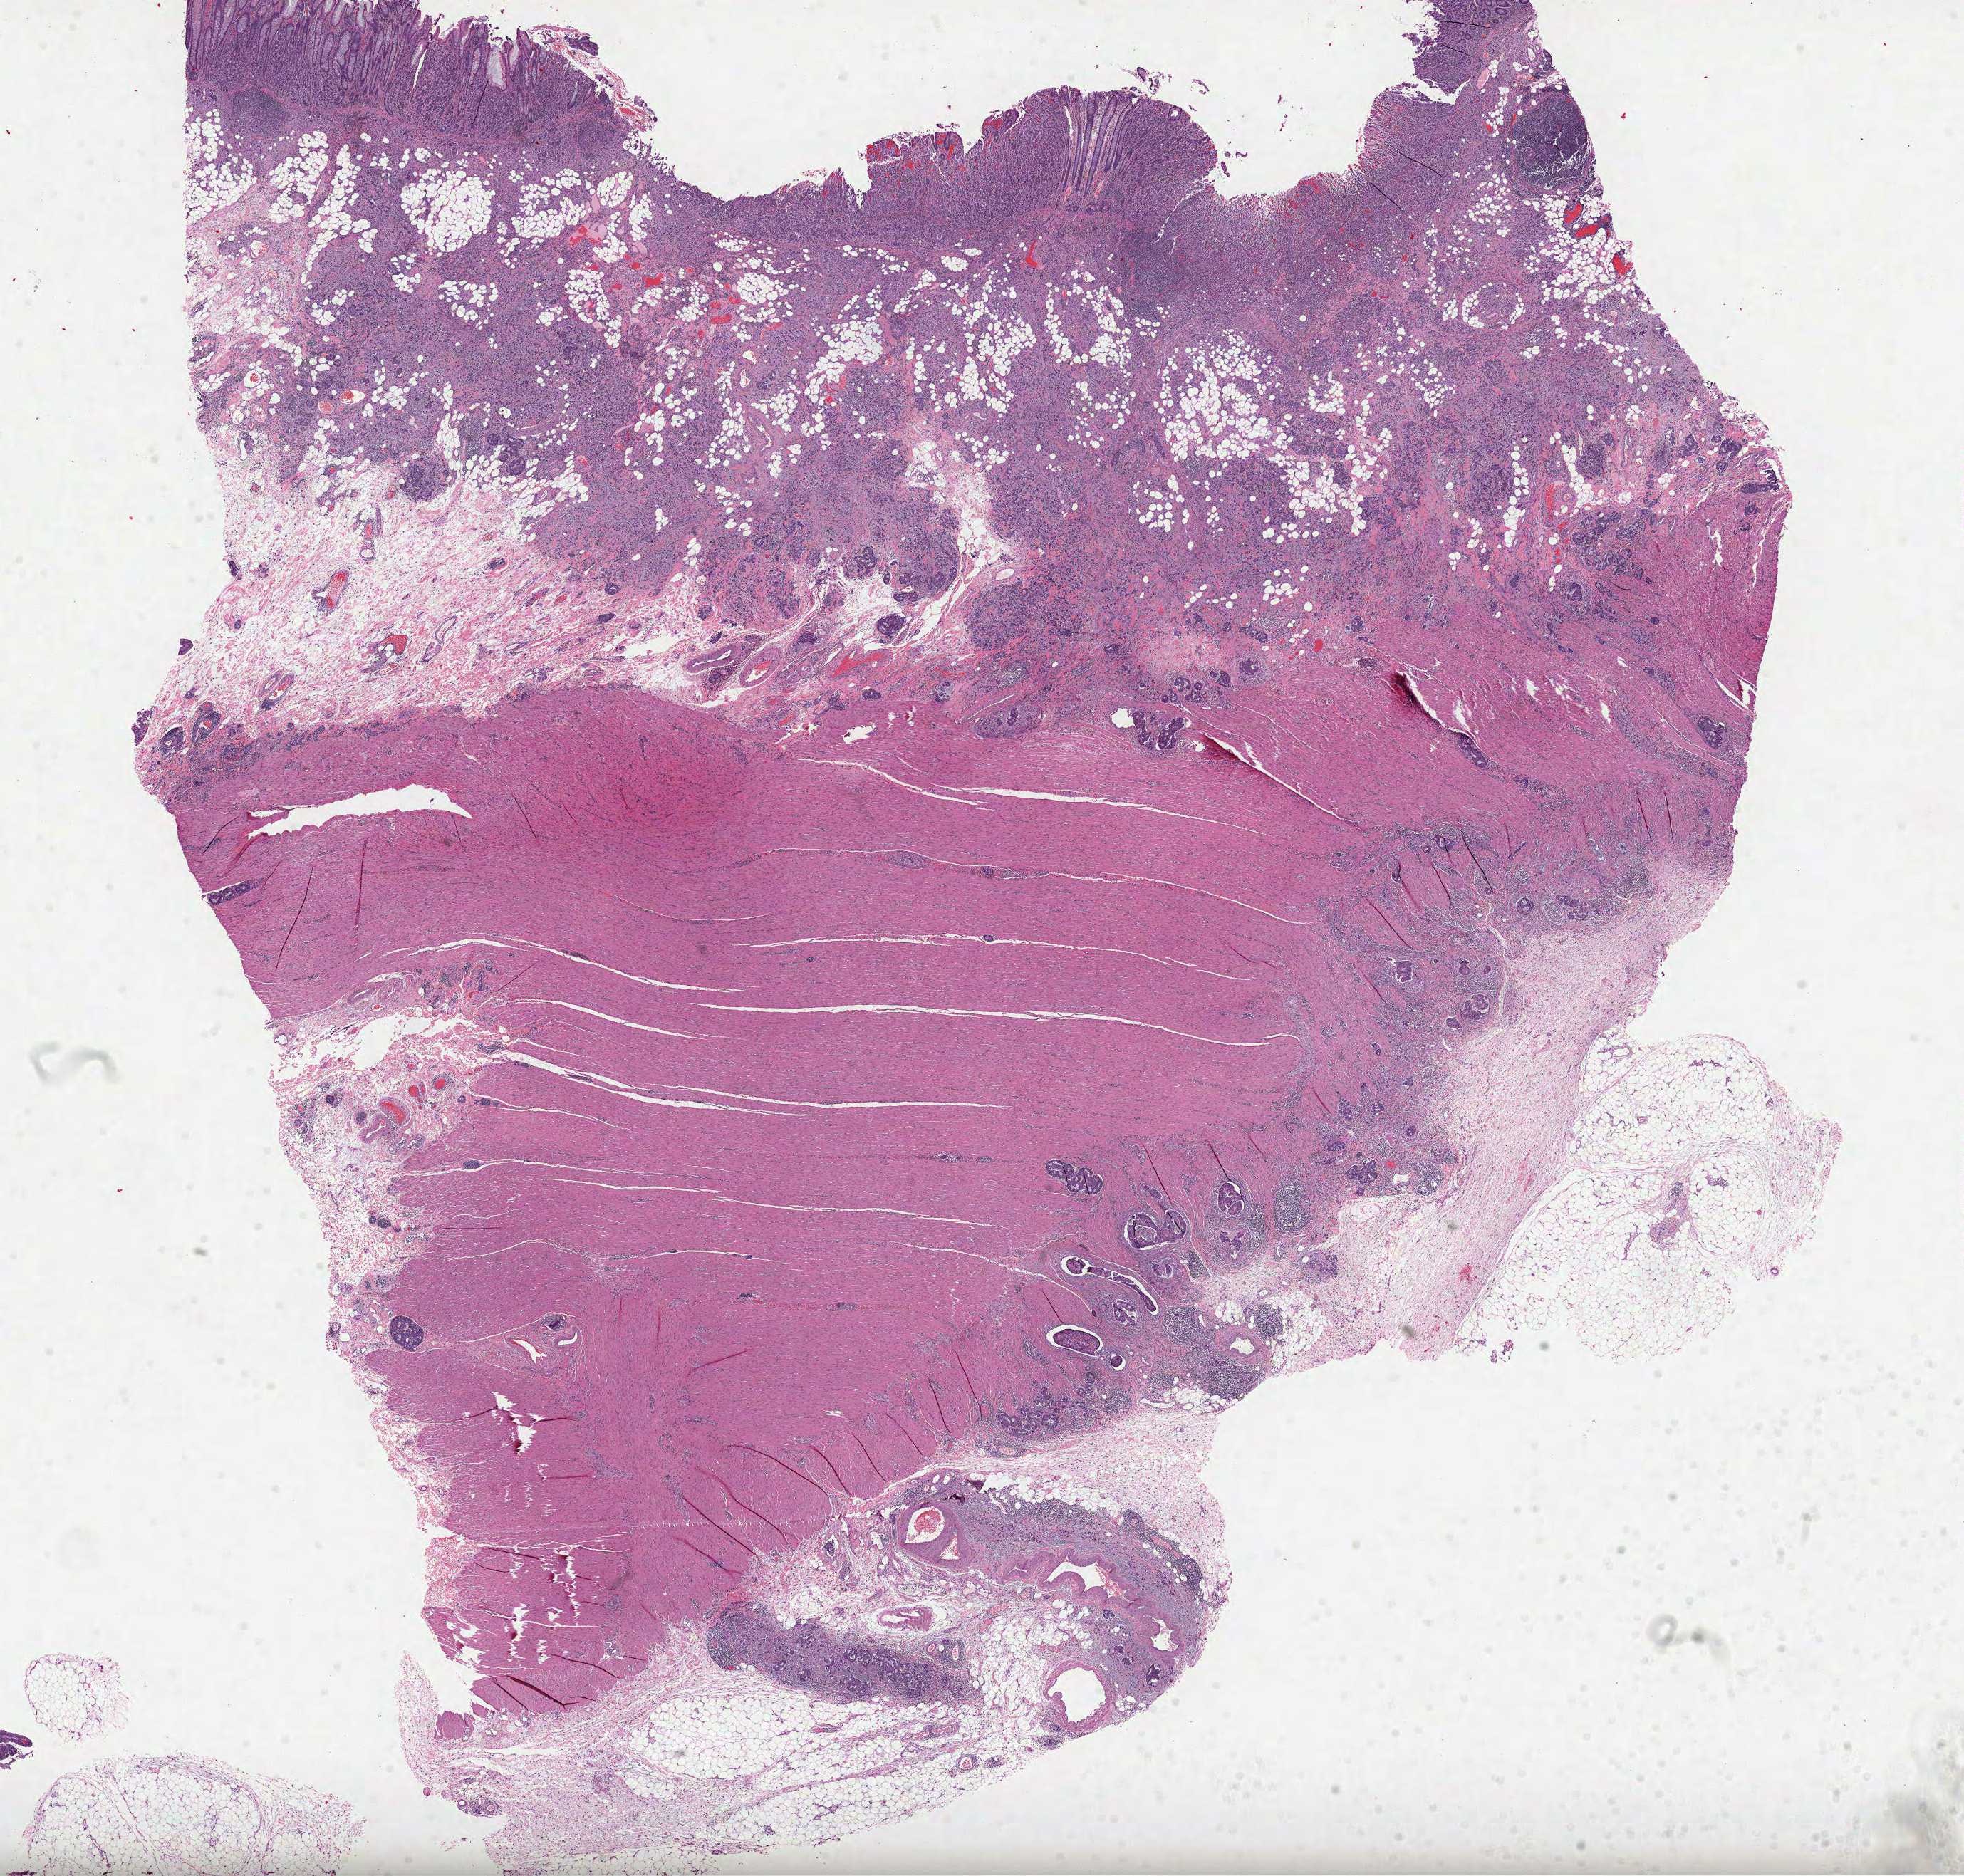
Whole-slide histology image, H&E-stained, shown as a low-resolution overview of the whole scanned area (about 22.2 x 21.2 mm). FFPE section. Colon, primary tumour sample. Female, age 57 years at initial diagnosis.
- AJCC pathologic stage: IIIC
- pathologic diagnosis: Adenocarcinoma, NOS